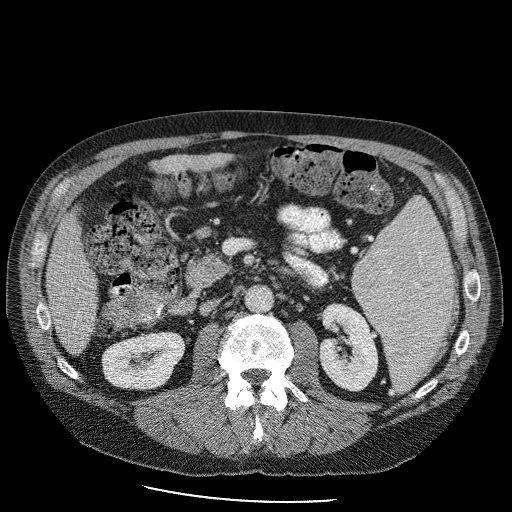
Contrast-enhanced abdominal CT (liver protocol), one axial slice. Slice 31 of 98 in the series (ordered by position). Reconstruction kernel STANDARD. 120 kVp. Soft-tissue window (W 400 / L 40 HU). 2.5 mm slice thickness. 512 × 512 image matrix. Case-level facts recorded for this patient, not image findings: diagnosis: hepatocellular carcinoma (patient treated with transarterial chemoembolisation; whether this scan precedes or follows treatment is not stated here); TNM stage (as recorded): Stage-II; Child-Pugh class: B; tumour differentiation: moderately differentiated.
Structures marked on this image (semi-automatic segmentation, software-assisted and operator-edited):
- liver parenchyma outside the tumour (the mass and vessels are separate outlines, so this box may not span the whole liver): bounding box [x1, y1, x2, y2] px = [46, 144, 266, 350]
- liver vessels: [78, 302, 81, 305]